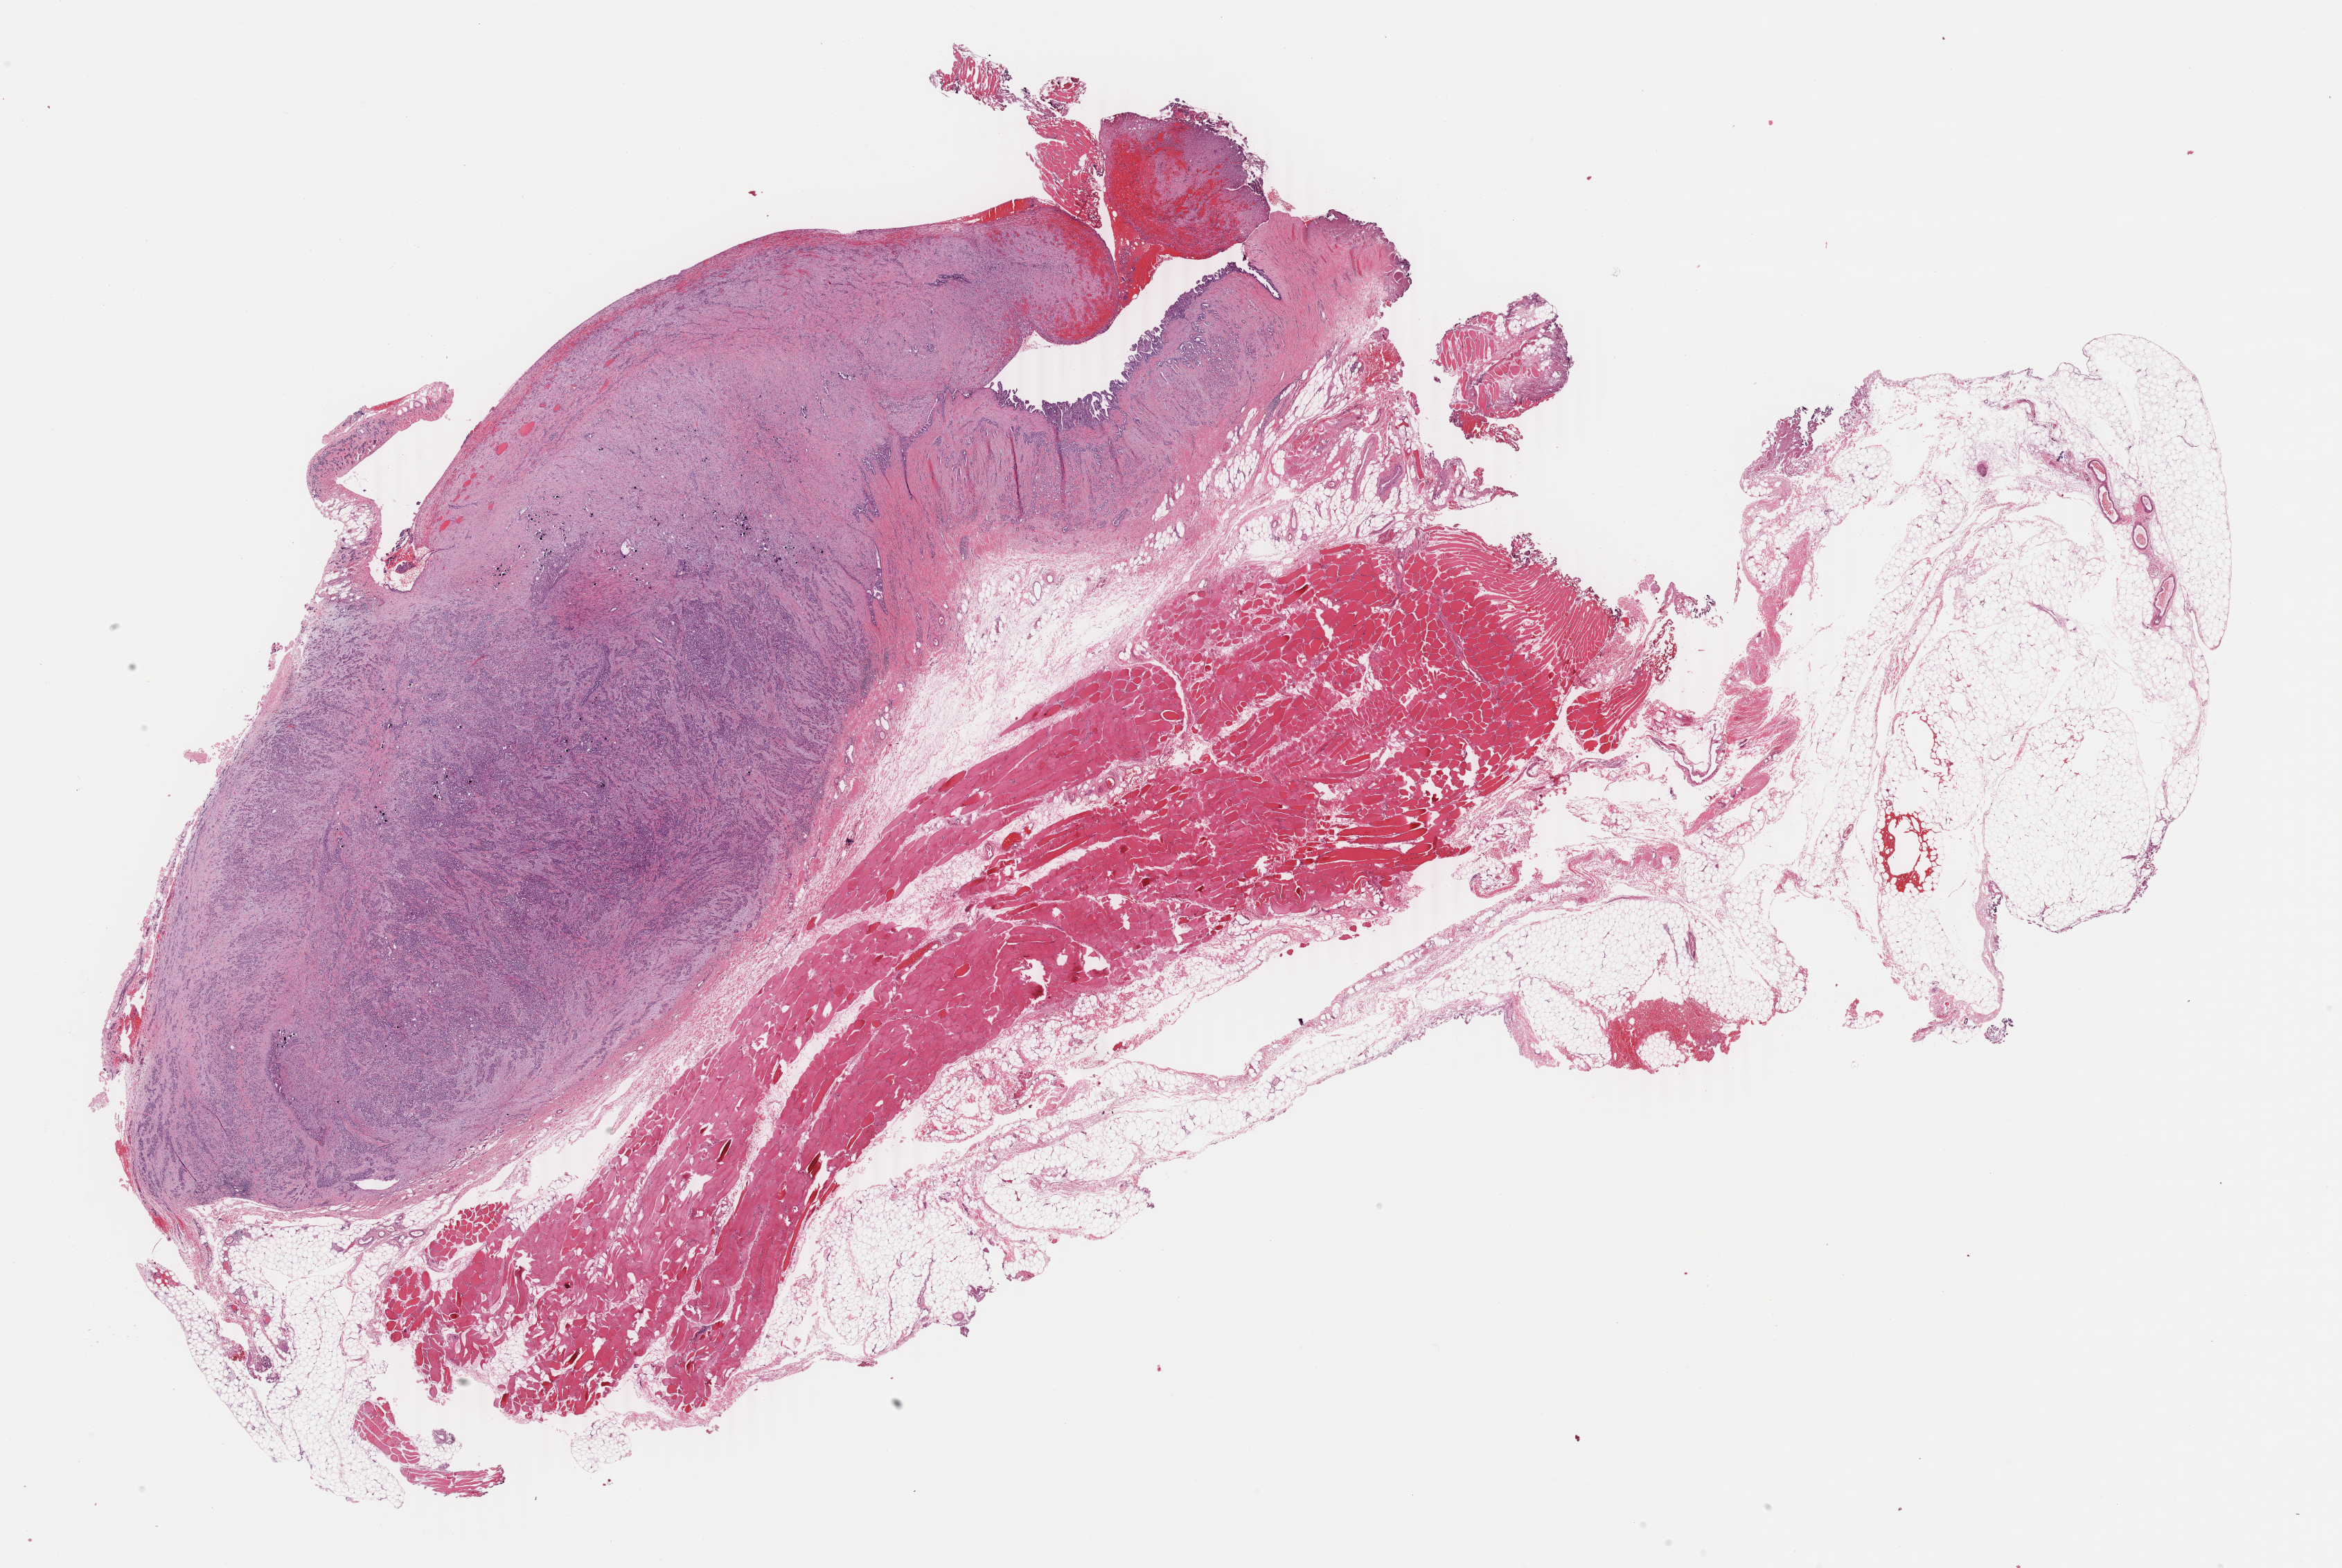
Digitized H&E tissue section (whole slide), a low-resolution overview of the entire scanned area, about 26.9 x 18.0 mm. Formalin-fixed paraffin-embedded (FFPE) diagnostic section. Sample: primary tumour, mesothelium. Patient: female, age at initial diagnosis 66 years.
AJCC pathologic stage: III (7th edition). Diagnosis: Mesothelioma, biphasic, malignant (pleura, NOS). Laterality: left.